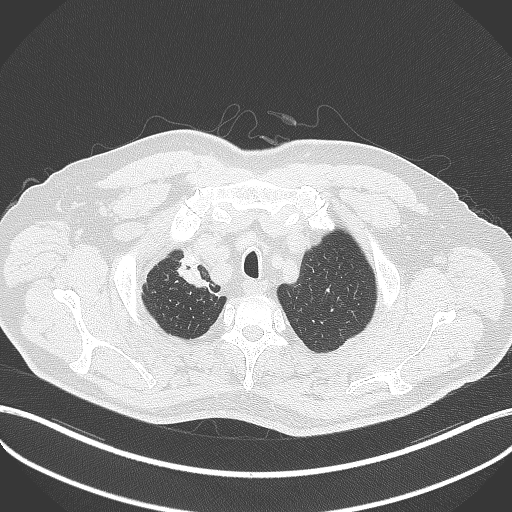
Chest CT, one axial slice. Position 340 of 411 along the scan axis. Reconstruction kernel B70f. 120 kVp. Lung window (W 1500 / L -600 HU). 1 mm slice thickness. 512 × 512 image matrix, field of view 400 × 400 mm. Male patient, age 60 years. From the clinical record (not read from this slice): clinical TNM (as recorded): T1b N1 M0.
Structures marked on this image (bounding box drawn by a radiologist):
- lung tumour (recorded histology: squamous cell carcinoma): bounding box <175,250,214,295> (left, top, right, bottom; pixels)